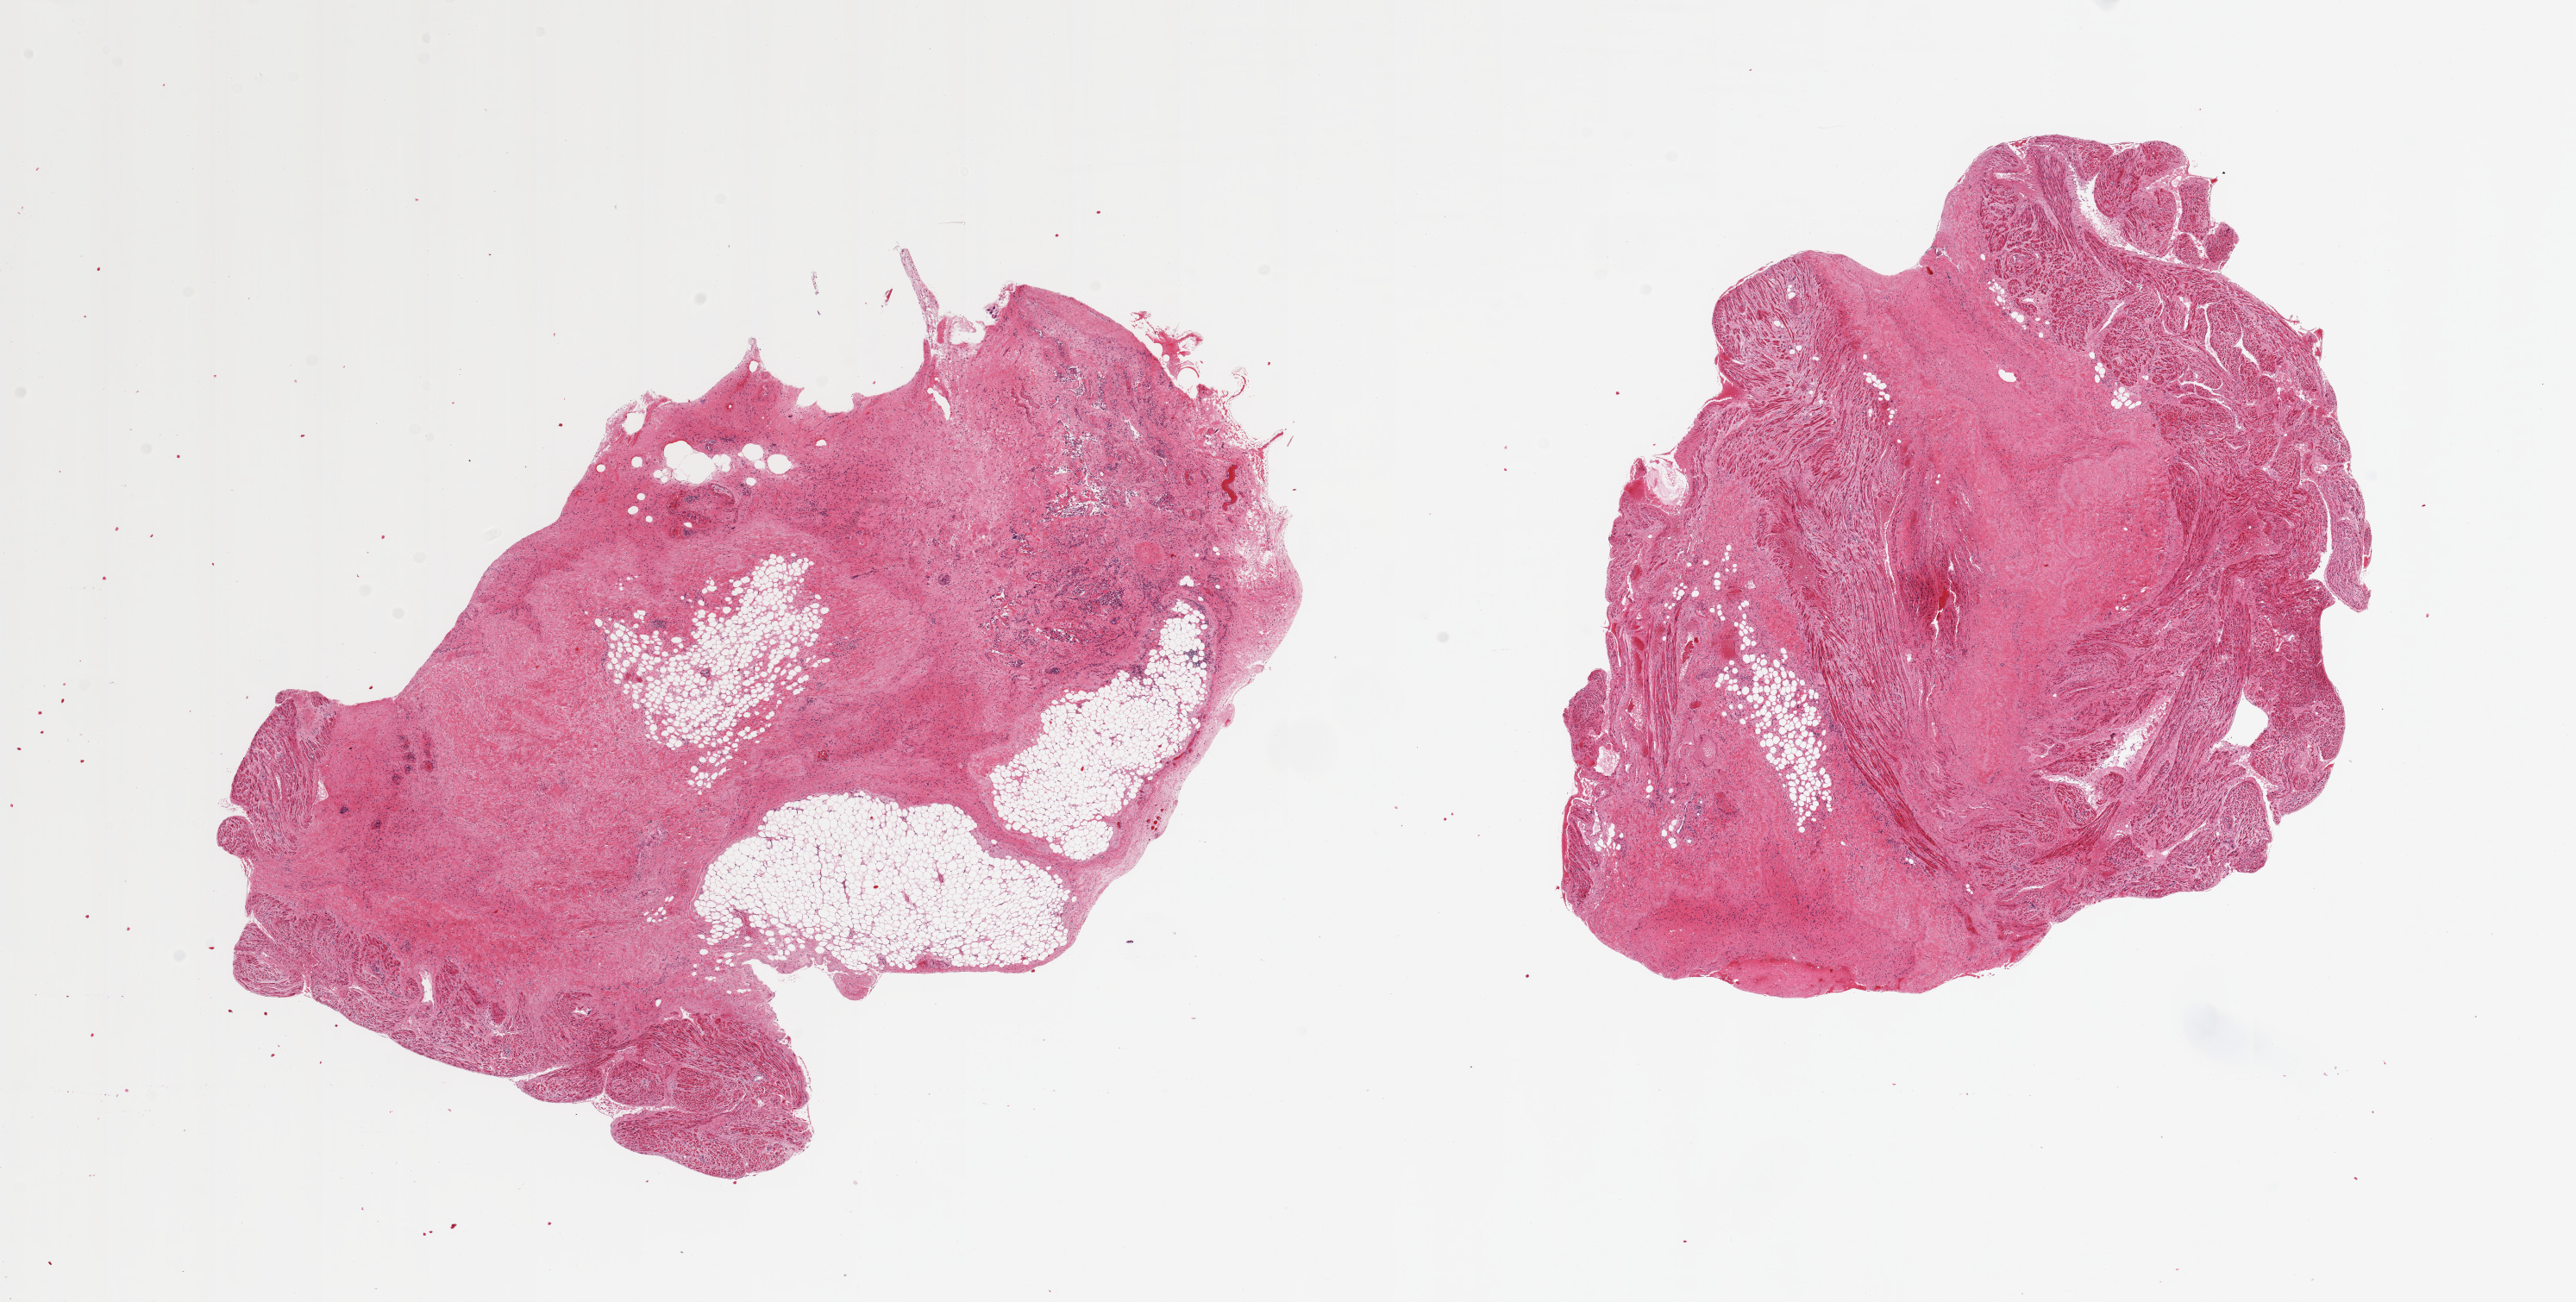
Digitized hematoxylin and eosin (H&E)-stained section — whole scanned area (about 23.6 x 11.9 mm, from a 20x scan) shown as a low-resolution overview, PAXgene-fixed, paraffin-embedded tissue, section of auricular appendage (target tissue), tissue donor sample. Female donor.
Reviewer comment on this tissue sample: 2 pieces, no abnormalities.